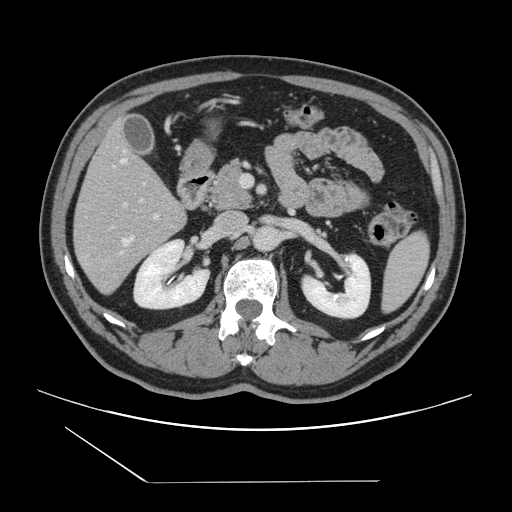
Contrast-enhanced abdominal CT, one axial slice; position 65 of 157 along the scan axis; soft-tissue window (W 400 / L 40 HU); 512 × 512 image matrix, field of view 407 × 407 mm. Male patient, age 61 years. Case-level facts recorded for this patient, not image findings: diagnosis: colorectal cancer liver metastases, imaged before liver resection; multiple liver metastases: yes; largest metastasis: 5.5 cm; disease in both lobes: yes.
Outlined on this slice (manually delineated by an expert):
- hepatic veins: bounding box <121,158,142,253> (left, top, right, bottom; pixels)
- liver: <75,126,185,294>
- planned liver remnant (the part of the liver to remain after resection): <76,125,176,218>
- portal vein (with intrahepatic branches): <112,165,158,228>